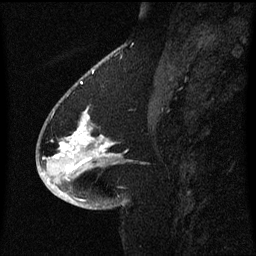
Breast MRI (dynamic contrast-enhanced), one sagittal slice; slice 25 of 60 in the series (ordered by position); dynamic contrast-enhanced series, image 2 of 3 at this slice position (ordered by acquisition); 1.5 T; TE 4.2 ms, TR 8.4 ms; 2 mm slice thickness; 256 × 256 image matrix. Female patient, age 54 years. Case-level facts recorded for this patient, not image findings: setting: breast cancer imaged before/during neoadjuvant chemotherapy; receptor status: HR-positive, HER2-negative.
Annotated regions visible in this slice (semi-automatic segmentation, software-assisted and operator-edited):
- analysis volume of interest (the breast-tissue region the enhancement analysis was run in; not a lesion): box from (x=46, y=102) to (x=121, y=171) px
- tumour enhancement mask (voxels above the 70 % enhancement threshold inside the analysis volume of interest): (x=71, y=110)–(x=111, y=151)